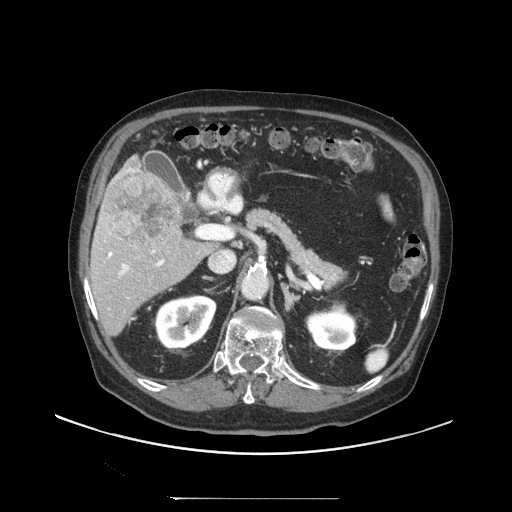
Contrast-enhanced abdominal CT (liver protocol), one axial slice; slice 55 of 97 in the series (ordered by position); 140 kVp; soft-tissue window (W 400 / L 40 HU); 512 × 512 image matrix, field of view 450 × 450 mm. From the clinical record (not read from this slice): diagnosis: hepatocellular carcinoma (patient treated with transarterial chemoembolisation; whether this scan precedes or follows treatment is not stated here); TNM stage (as recorded): Stage-IIIC; Child-Pugh class: A; tumour differentiation: well differentiated; tumour nodularity: uninodular.
Annotated regions visible in this slice (semi-automatically segmented with operator editing):
- liver parenchyma outside the tumour (the mass and vessels are separate outlines, so this box may not span the whole liver): bounding box [x1, y1, x2, y2] px = [90, 156, 210, 336]
- mass: [104, 171, 181, 247]
- liver vessels: [108, 168, 164, 276]